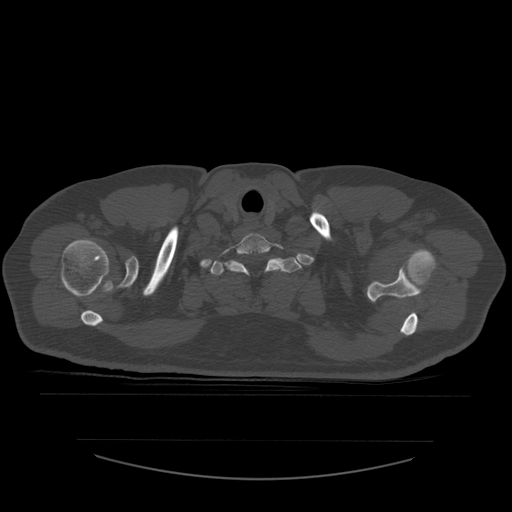
CT including the spine, one axial slice; reconstruction kernel STANDARD; 120 kVp; bone window (W 1800 / L 400 HU); 512 × 512 image matrix. Patient age 44 years. From the clinical record (not read from this slice): primary cancer: soft tissue sarcoma.
Annotated regions visible in this slice (semi-automatically segmented with operator editing):
- T1 vertebra: box from (x=211, y=258) to (x=302, y=276) px